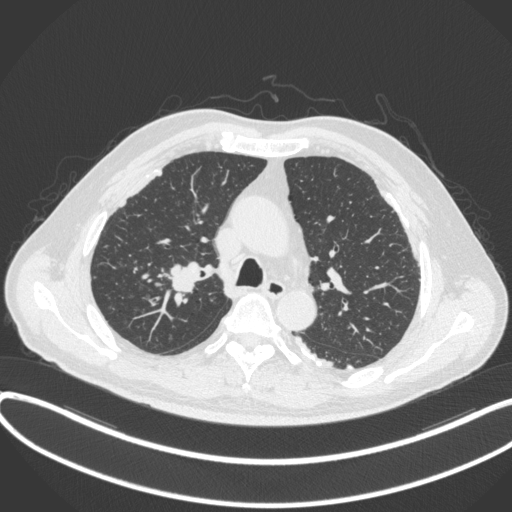
Chest CT, one axial slice. Position 291 of 455 along the scan axis. Reconstruction kernel B31f. 120 kVp. Lung window (W 1500 / L -600 HU). 1 mm slice thickness. 512 × 512 image matrix, field of view 400 × 400 mm. Male patient, age 58 years. Case-level facts recorded for this patient, not image findings: clinical TNM (as recorded): T1c N0 M0.
Annotated regions visible in this slice (rectangle marked by the reading radiologist):
- lung tumour (recorded histology: squamous cell carcinoma): box from (x=163, y=259) to (x=204, y=294) px